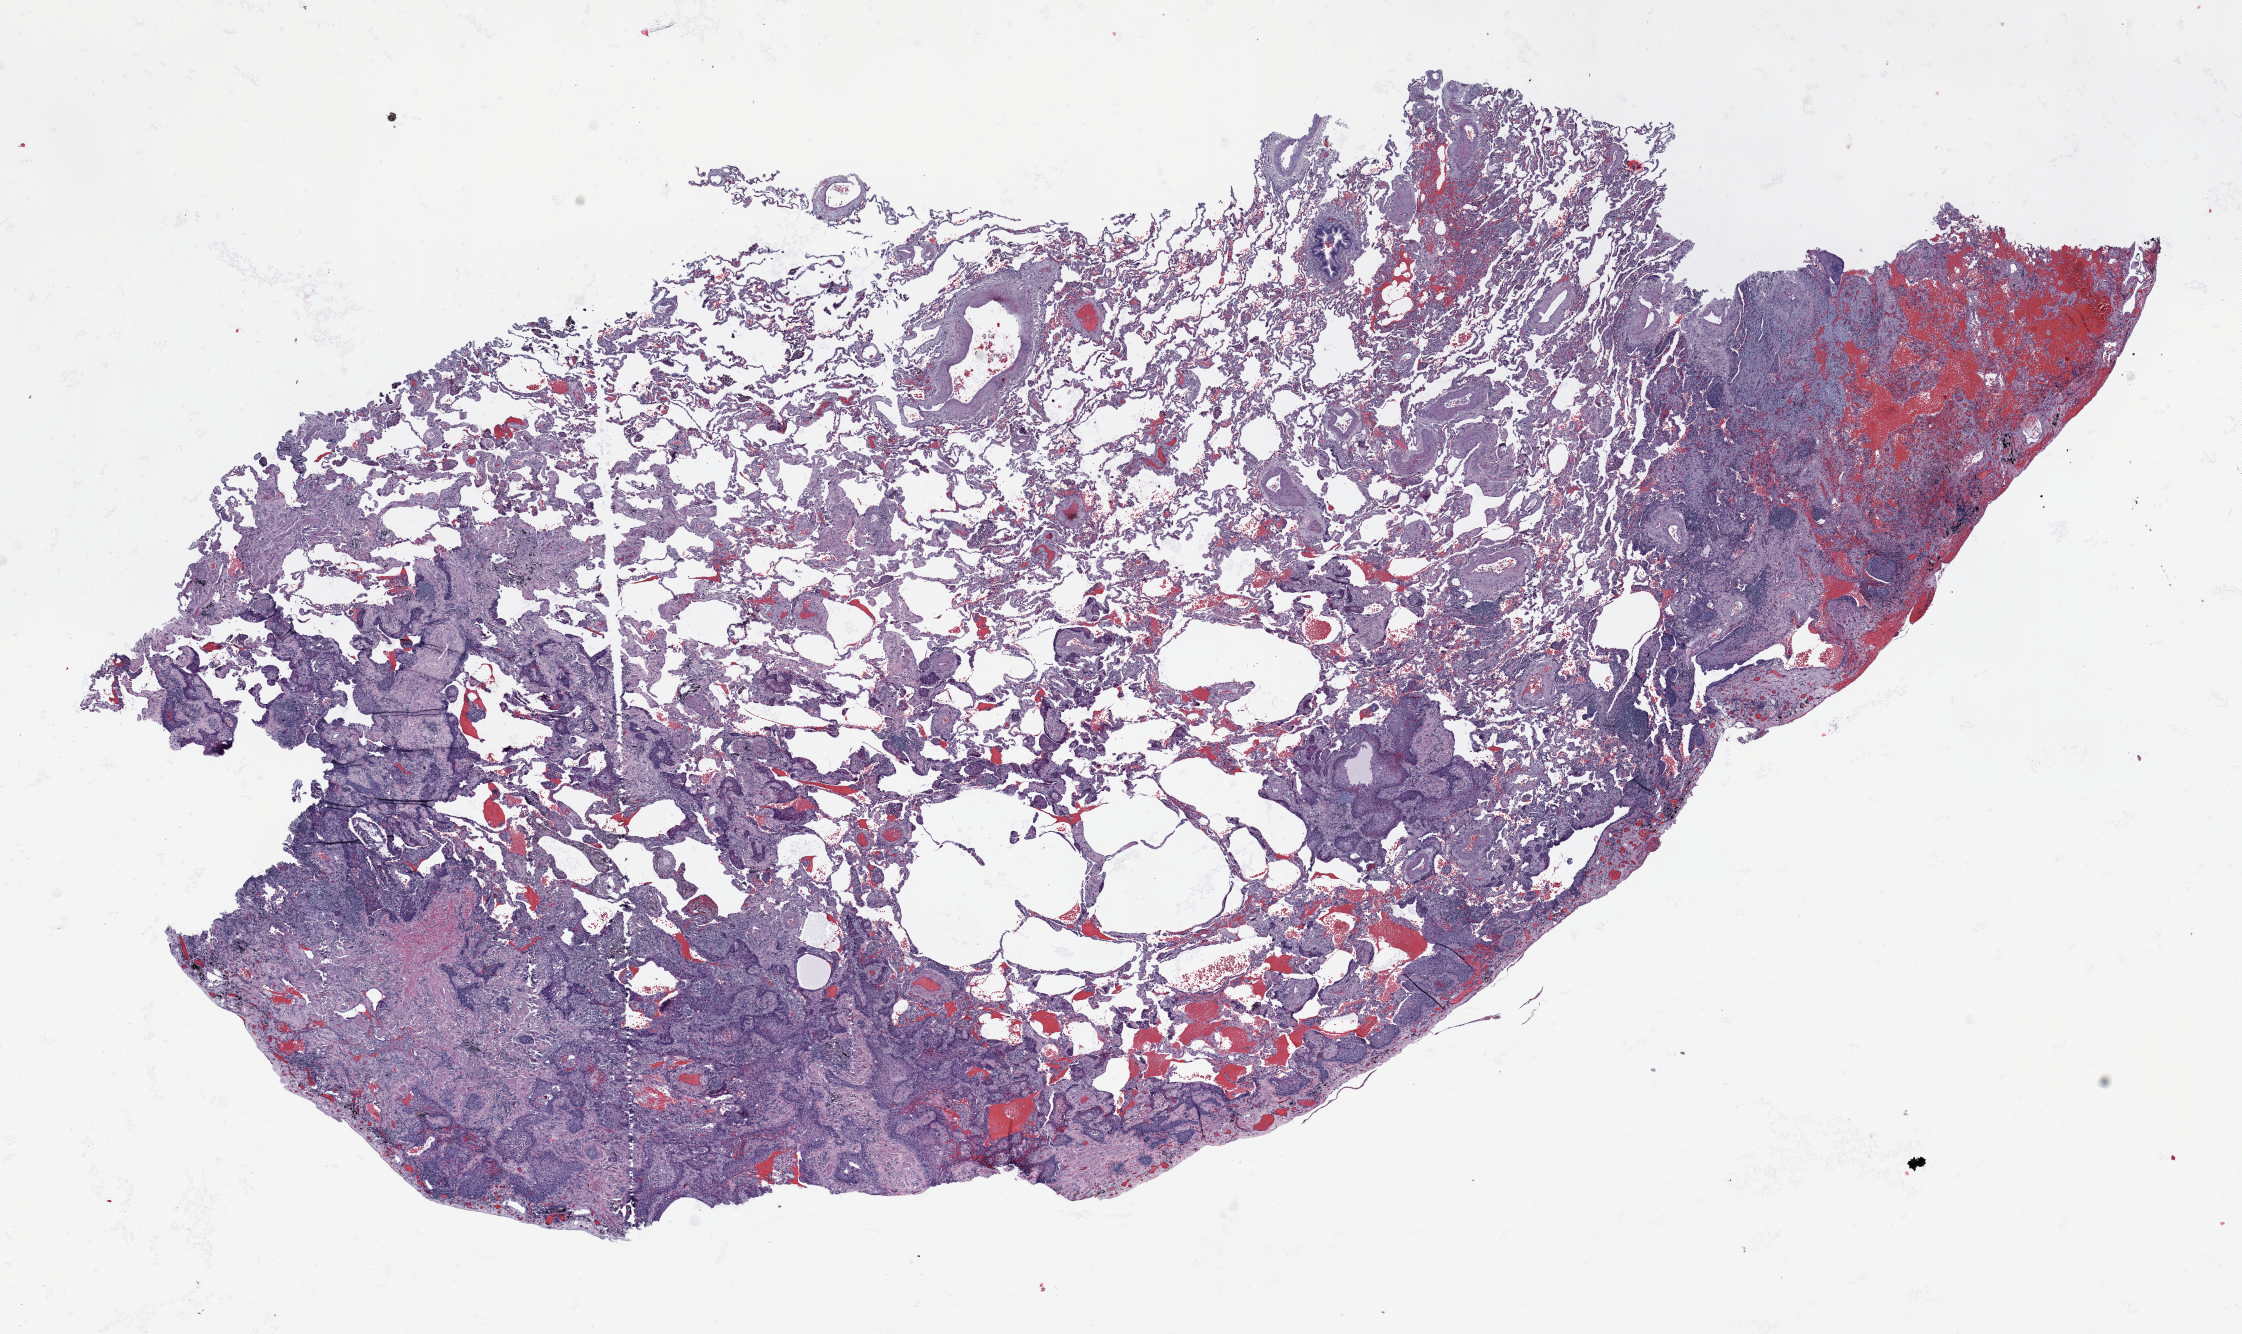
H&E whole-slide image — a low-resolution overview of the entire scanned area, about 18.0 x 10.7 mm. FFPE section. Lung tissue. Female, age 70 at enrolment. Current smoker at enrolment. Grade: well differentiated (G1).
Participant's lung-cancer diagnosis: Squamous cell carcinoma, NOS. Tumour size (pathology): 25 mm. Primary tumour location (clinical record): right lower lobe. Stage (AJCC 6th edition): IA.